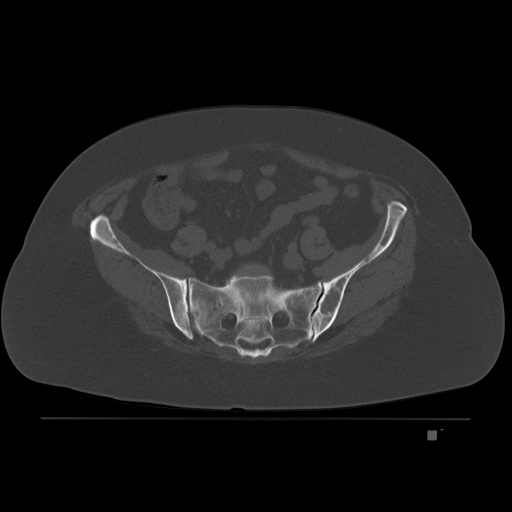
CT including the spine, one axial slice; slice 19 of 221 in the series (ordered by position); bone window (W 1800 / L 400 HU); 512 × 512 image matrix, field of view 474 × 474 mm. Patient: female, 63 years. Case-level facts recorded for this patient, not image findings: primary cancer: breast.
Structures marked on this image (semi-automatic segmentation, software-assisted and operator-edited):
- L5 vertebra: bounding box <248,264,257,268> (left, top, right, bottom; pixels)